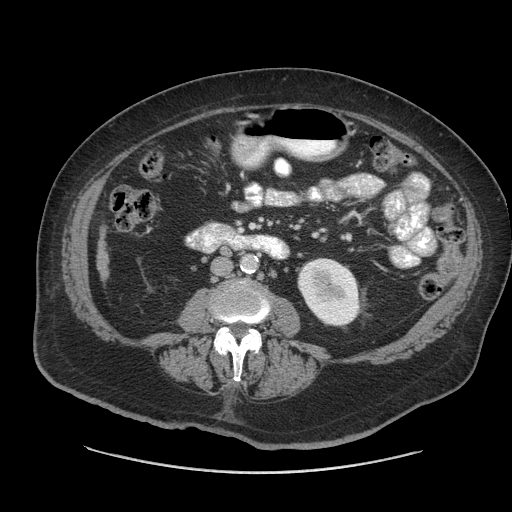
Contrast-enhanced abdominal CT (liver protocol), one axial slice. Position 8 of 91 along the scan axis. 140 kVp. Soft-tissue window (W 400 / L 40 HU). 2.5 mm slice thickness. 512 × 512 image matrix, field of view 420 × 420 mm. Case-level facts recorded for this patient, not image findings: diagnosis: hepatocellular carcinoma (patient treated with transarterial chemoembolisation; whether this scan precedes or follows treatment is not stated here); TNM stage (as recorded): Stage-I; Child-Pugh class: A.
Outlined on this slice (semi-automatically segmented with operator editing):
- liver parenchyma outside the tumour (the mass and vessels are separate outlines, so this box may not span the whole liver): bounding box [x1, y1, x2, y2] px = [96, 231, 108, 280]